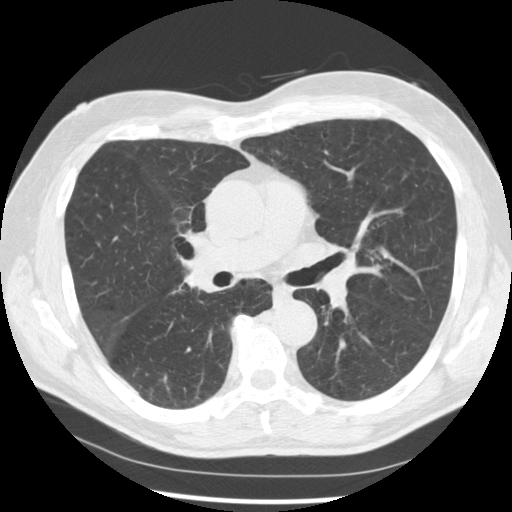
Low-dose screening chest CT, one axial slice. Slice 162 of 277 in the series (ordered by position). Lung window (W 1500 / L -600 HU). 2.5 mm slice thickness. 512 × 512 image matrix.
Structures marked on this image (expert manual segmentation):
- lesion 1 (tumor, middle lobe of right lung): bounding box <183,261,219,293> (left, top, right, bottom; pixels)